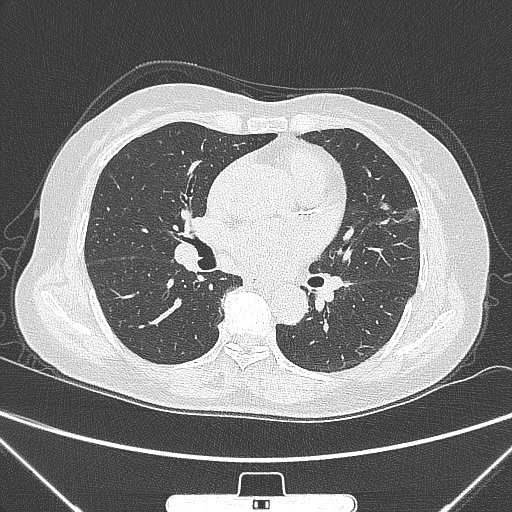
Chest CT, one axial slice. Slice 144 of 300 in the series (ordered by position). 120 kVp. Lung window (W 1500 / L -600 HU). 512 × 512 image matrix, field of view 350 × 350 mm. Patient: female, 70 years. Case-level facts recorded for this patient, not image findings: clinical TNM (as recorded): T1b N0 M0.
Structures marked on this image (bounding box drawn by a radiologist):
- lung tumour (recorded histology: adenocarcinoma): bounding box (x1, y1, x2, y2) in pixels: (377, 198, 395, 222)